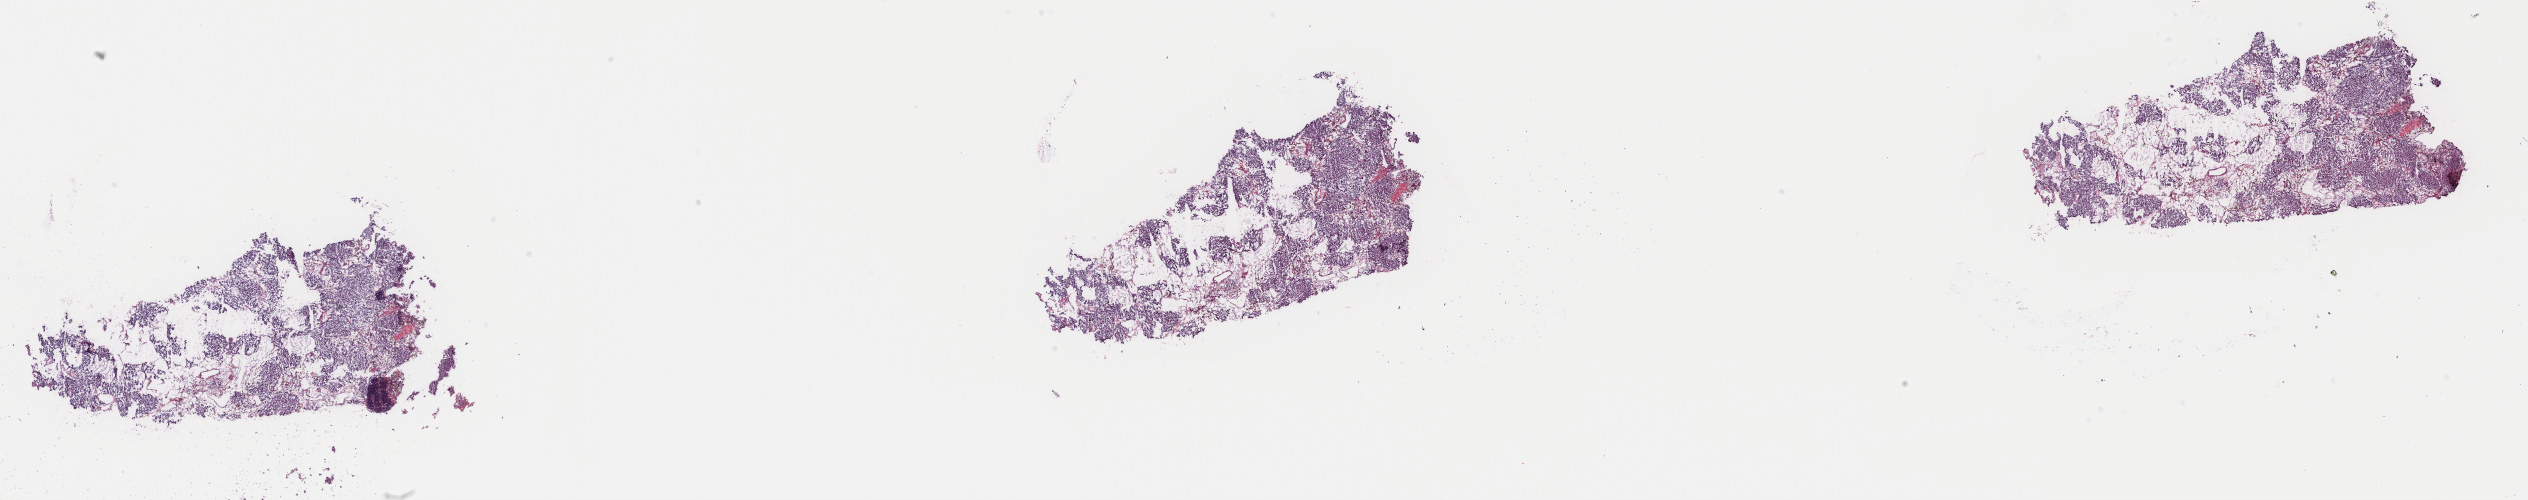
Digitized H&E-stained tissue section (whole slide), low-resolution overview of the scanned area, about 40.1 x 7.9 mm (slide scanned at 40x). Frozen section from the top of the tissue portion. Primary tumour sample from the adrenal gland. Female, age 47 years at initial diagnosis. Slide review estimates, as recorded: tumour cells 100%, tumour nuclei 75%.
Pathologic diagnosis: Pheochromocytoma, NOS.